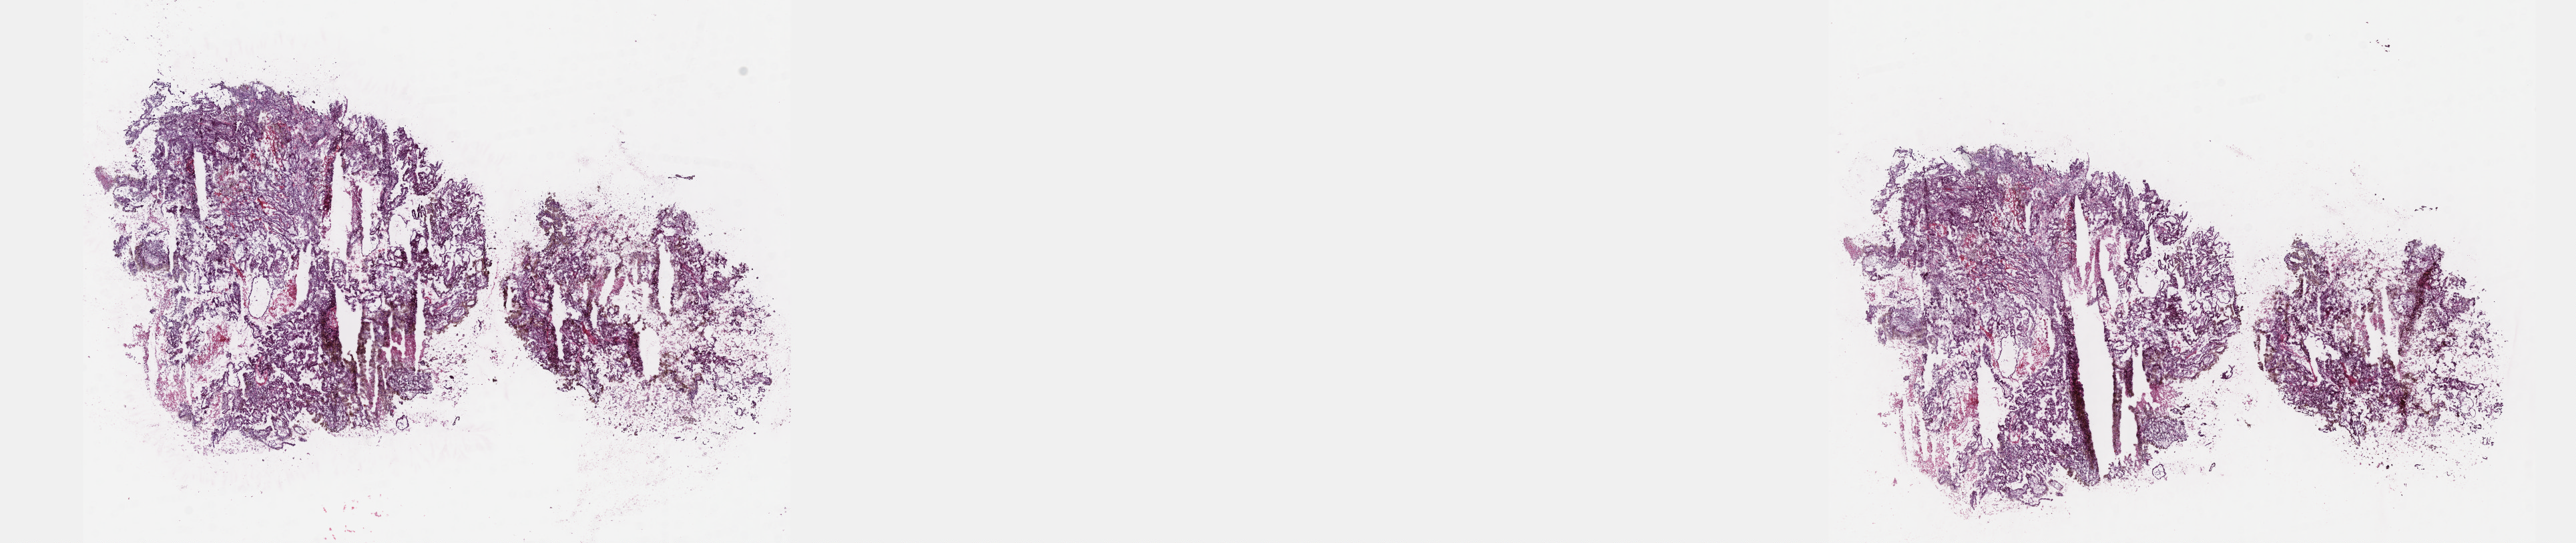
Whole-slide histology image, Hematoxylin and eosin (H&E) stained, a low-resolution overview of the entire scanned area, about 31.2 x 6.6 mm (acquisition: 40x scan); frozen section from the top of the tissue portion; sample: primary tumour, kidney. Male patient; age at initial diagnosis 70 years. Slide review estimates, as recorded: tumour cells 80%, tumour nuclei 80%.
Pathologic diagnosis: Papillary adenocarcinoma, NOS.